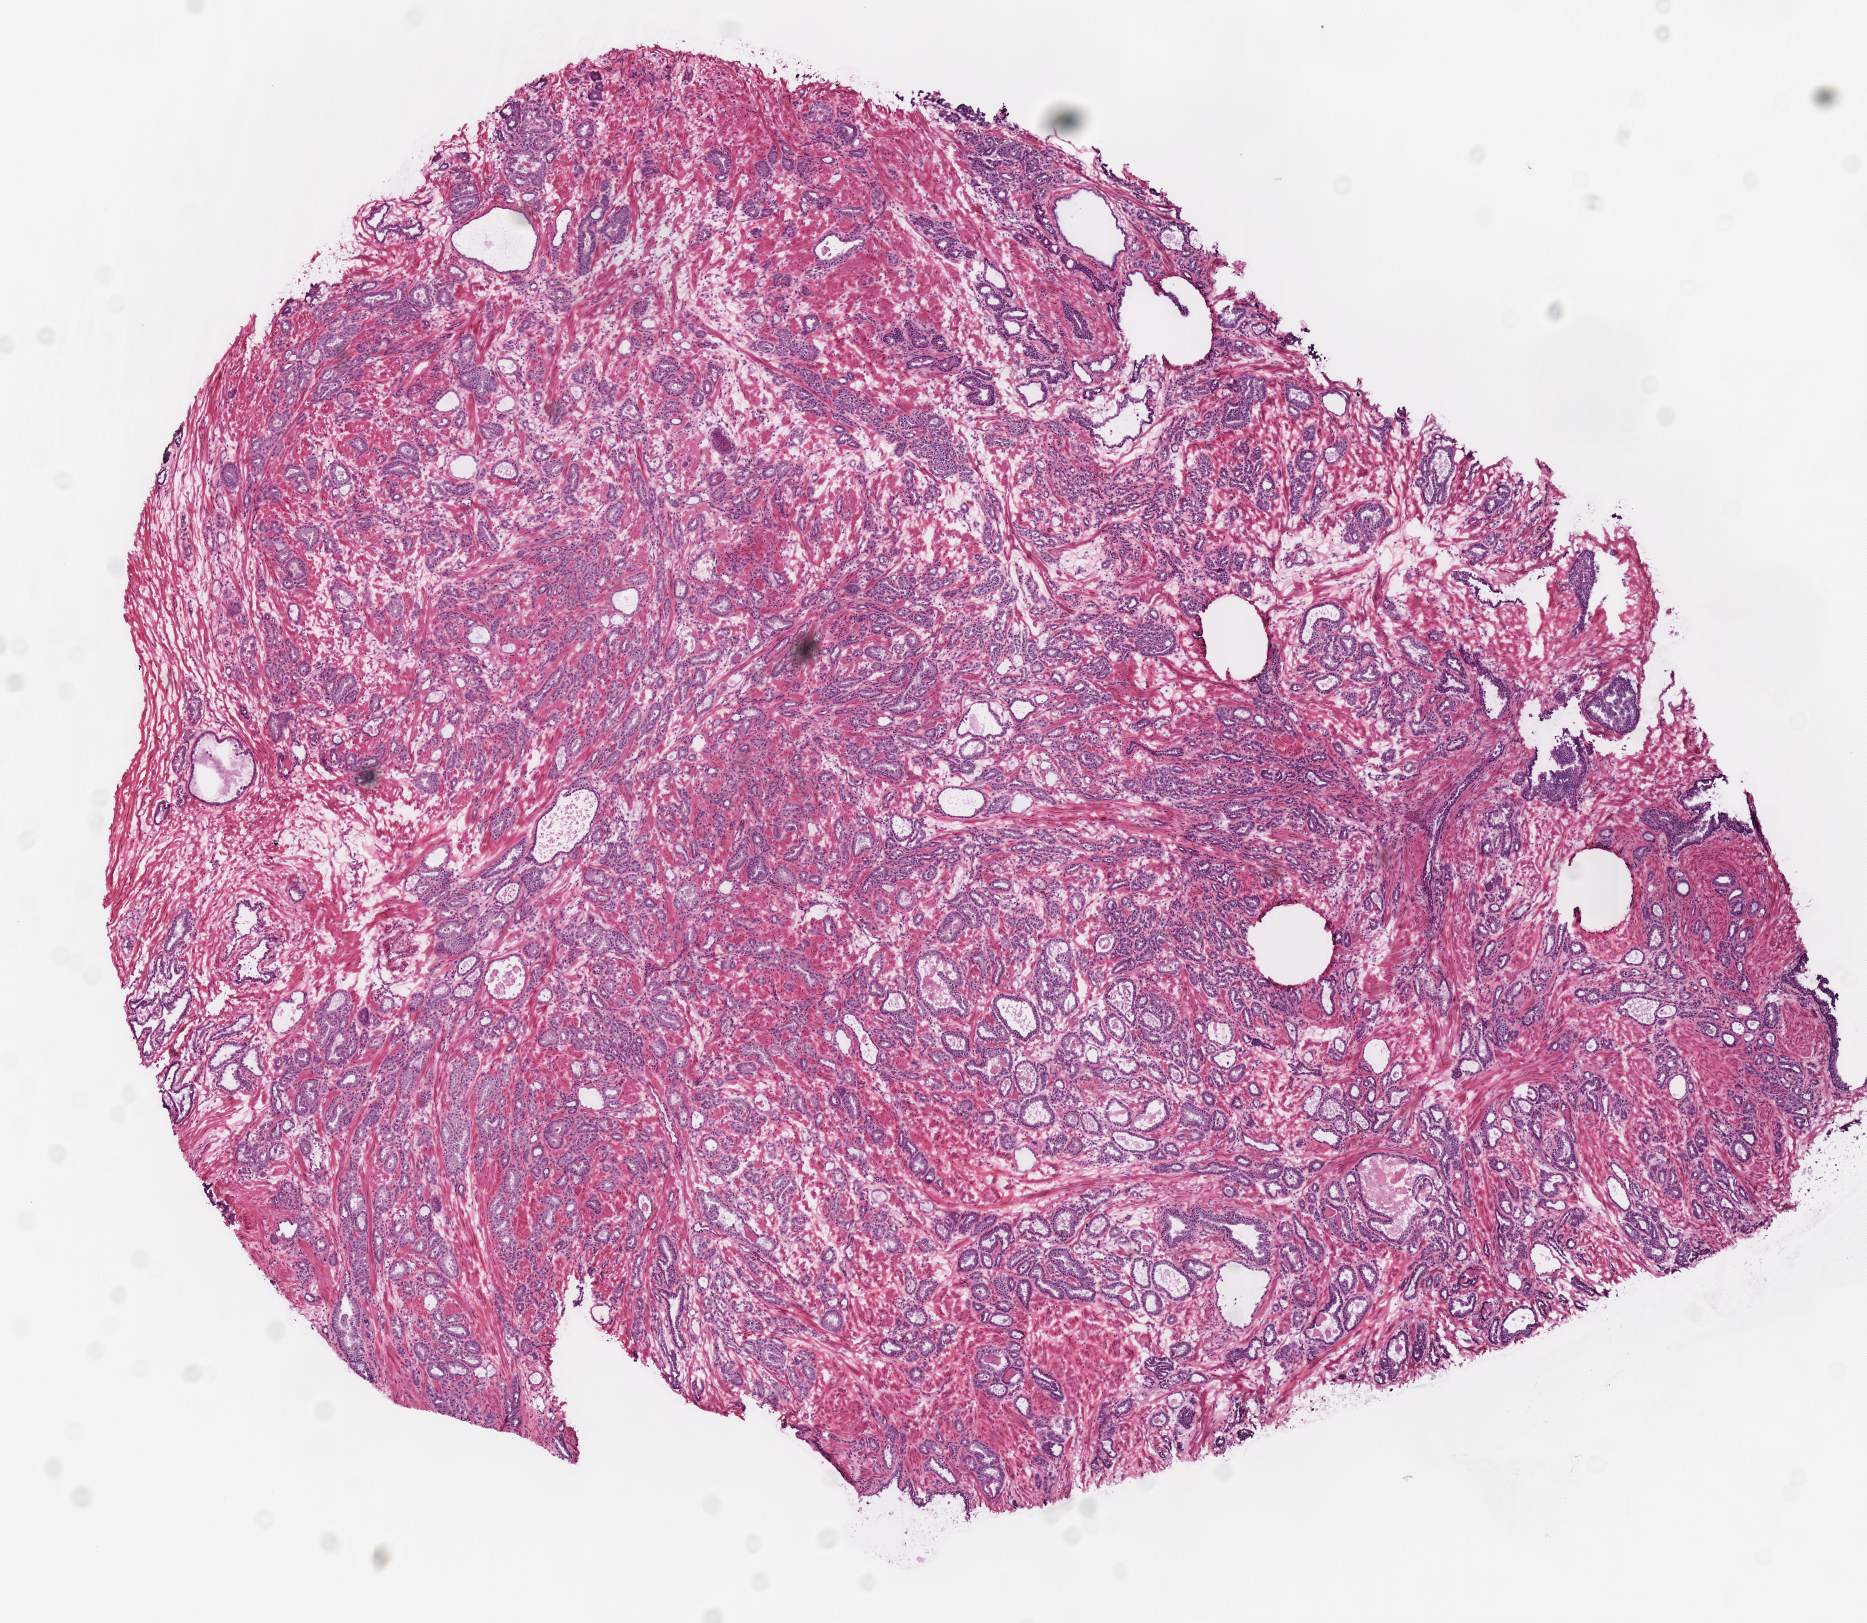
Digitized Hematoxylin and eosin (H&E) stained tissue section (whole slide) — whole scanned area (about 7.3 x 6.4 mm, slide scanned at 40x) shown as a low-resolution overview; frozen section from the top of the tissue portion; prostate, primary tumour sample. Male patient; age at initial diagnosis 59 years. Gleason score: 7 (3+4). Slide review estimates, as recorded: tumour nuclei 65%, necrosis 0%.
• pathologic diagnosis: Acinar cell carcinoma (prostate gland)
• lymph nodes positive (case pathology): 0 of 4 examined